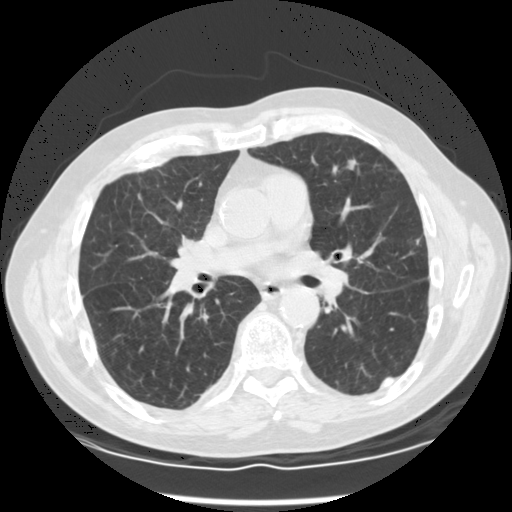
Chest CT (low-dose screening protocol), one axial image. Third annual screen. Lung window (W 1500 / L -600 HU). Slice 63 of 120 in the series. Male participant, aged 68 years at enrolment.
Lesion marked by an expert reader, bounding box <326,147,373,191> (left, top, right, bottom; pixels). Reader record for this screening exam (exam-level; its link to the box is not recorded): non-calcified nodule or mass ≥4 mm, left upper lobe, 10 × 8 mm, spiculated (stellate) margins, soft tissue attenuation, pre-existing on the prior screen: no. Later outcome: lung cancer diagnosed 53 days after this screen — squamous cell carcinoma, NOS, left upper lobe, moderately differentiated (G2), stage IA (AJCC 6th edition), 17 mm at pathology.